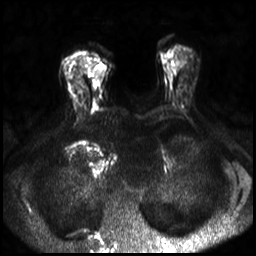
Breast MRI, one axial slice. Position 12 of 30 along the scan axis. Diffusion-weighted series; image 2 of 4 stored at this slice position (different b-values; order by instance number). 3 T. 256 × 256 image matrix, field of view 320 × 320 mm. Female patient.
Annotated regions visible in this slice (expert manual segmentation):
- tumour on diffusion-weighted imaging: bounding box [x1, y1, x2, y2] px = [95, 65, 105, 78]